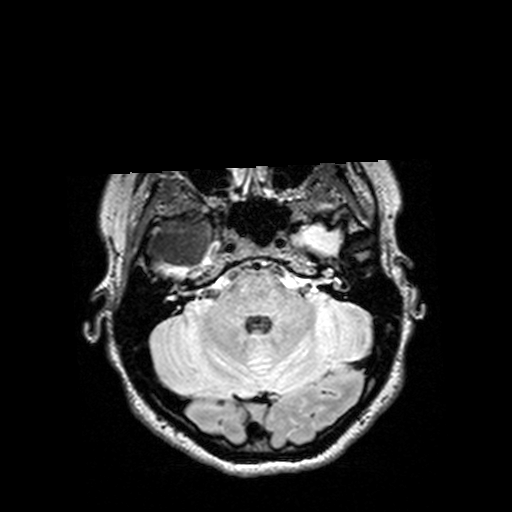
Brain MRI from a brain-tumour surgery series, one axial slice. Slice 108 of 144 in the series (ordered by position). T2 FLAIR. 512 × 512 image matrix, field of view 250 × 250 mm. Case-level facts recorded for this patient, not image findings: histopathology: Astrocytoma; WHO grade: 3; IDH mutation: yes; tumour location: Right Insular Temporal.
Structures marked on this image (outlined manually by an expert reader):
- tumour: box from (x=129, y=219) to (x=191, y=271) px